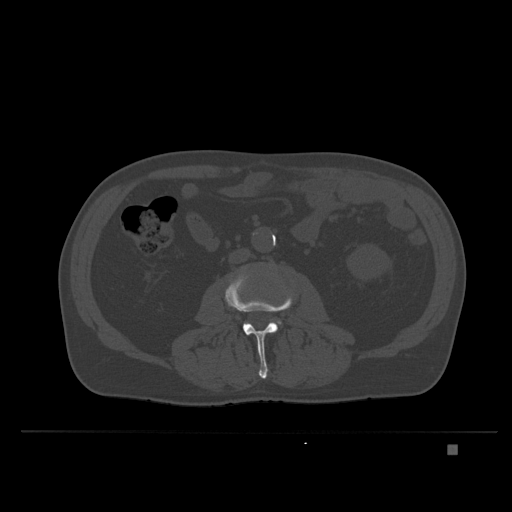
CT including the spine, one axial slice; slice 93 of 435 in the series (ordered by position); bone window (W 1800 / L 400 HU); 1.5 mm slice thickness; 512 × 512 image matrix, field of view 434 × 434 mm. Male patient, age 73 years. From the clinical record (not read from this slice): primary cancer: skin.
Annotated regions visible in this slice (semi-automatic segmentation, software-assisted and operator-edited):
- L3 vertebra: bounding box [x1, y1, x2, y2] px = [225, 272, 294, 379]
- L4 vertebra: [271, 319, 280, 322]